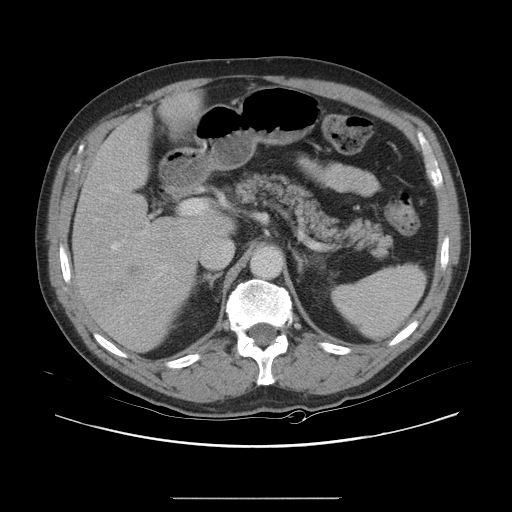
Contrast-enhanced abdominal CT, one axial slice. Position 14 of 40 along the scan axis. Intravenous contrast given. Soft-tissue window (W 400 / L 40 HU). 5 mm slice thickness. 512 × 512 image matrix, field of view 408 × 408 mm. Male patient, age 64 years. Case-level facts recorded for this patient, not image findings: diagnosis: colorectal cancer liver metastases, imaged before liver resection; multiple liver metastases: yes; largest metastasis: 3.2 cm; disease in both lobes: yes.
Annotated regions visible in this slice (outlined manually by an expert reader):
- hepatic veins: bounding box <112,191,125,250> (left, top, right, bottom; pixels)
- liver: <75,98,227,352>
- planned liver remnant (the part of the liver to remain after resection): <88,99,227,240>
- portal vein (with intrahepatic branches): <184,201,194,214>
- liver metastasis: <109,265,140,299>